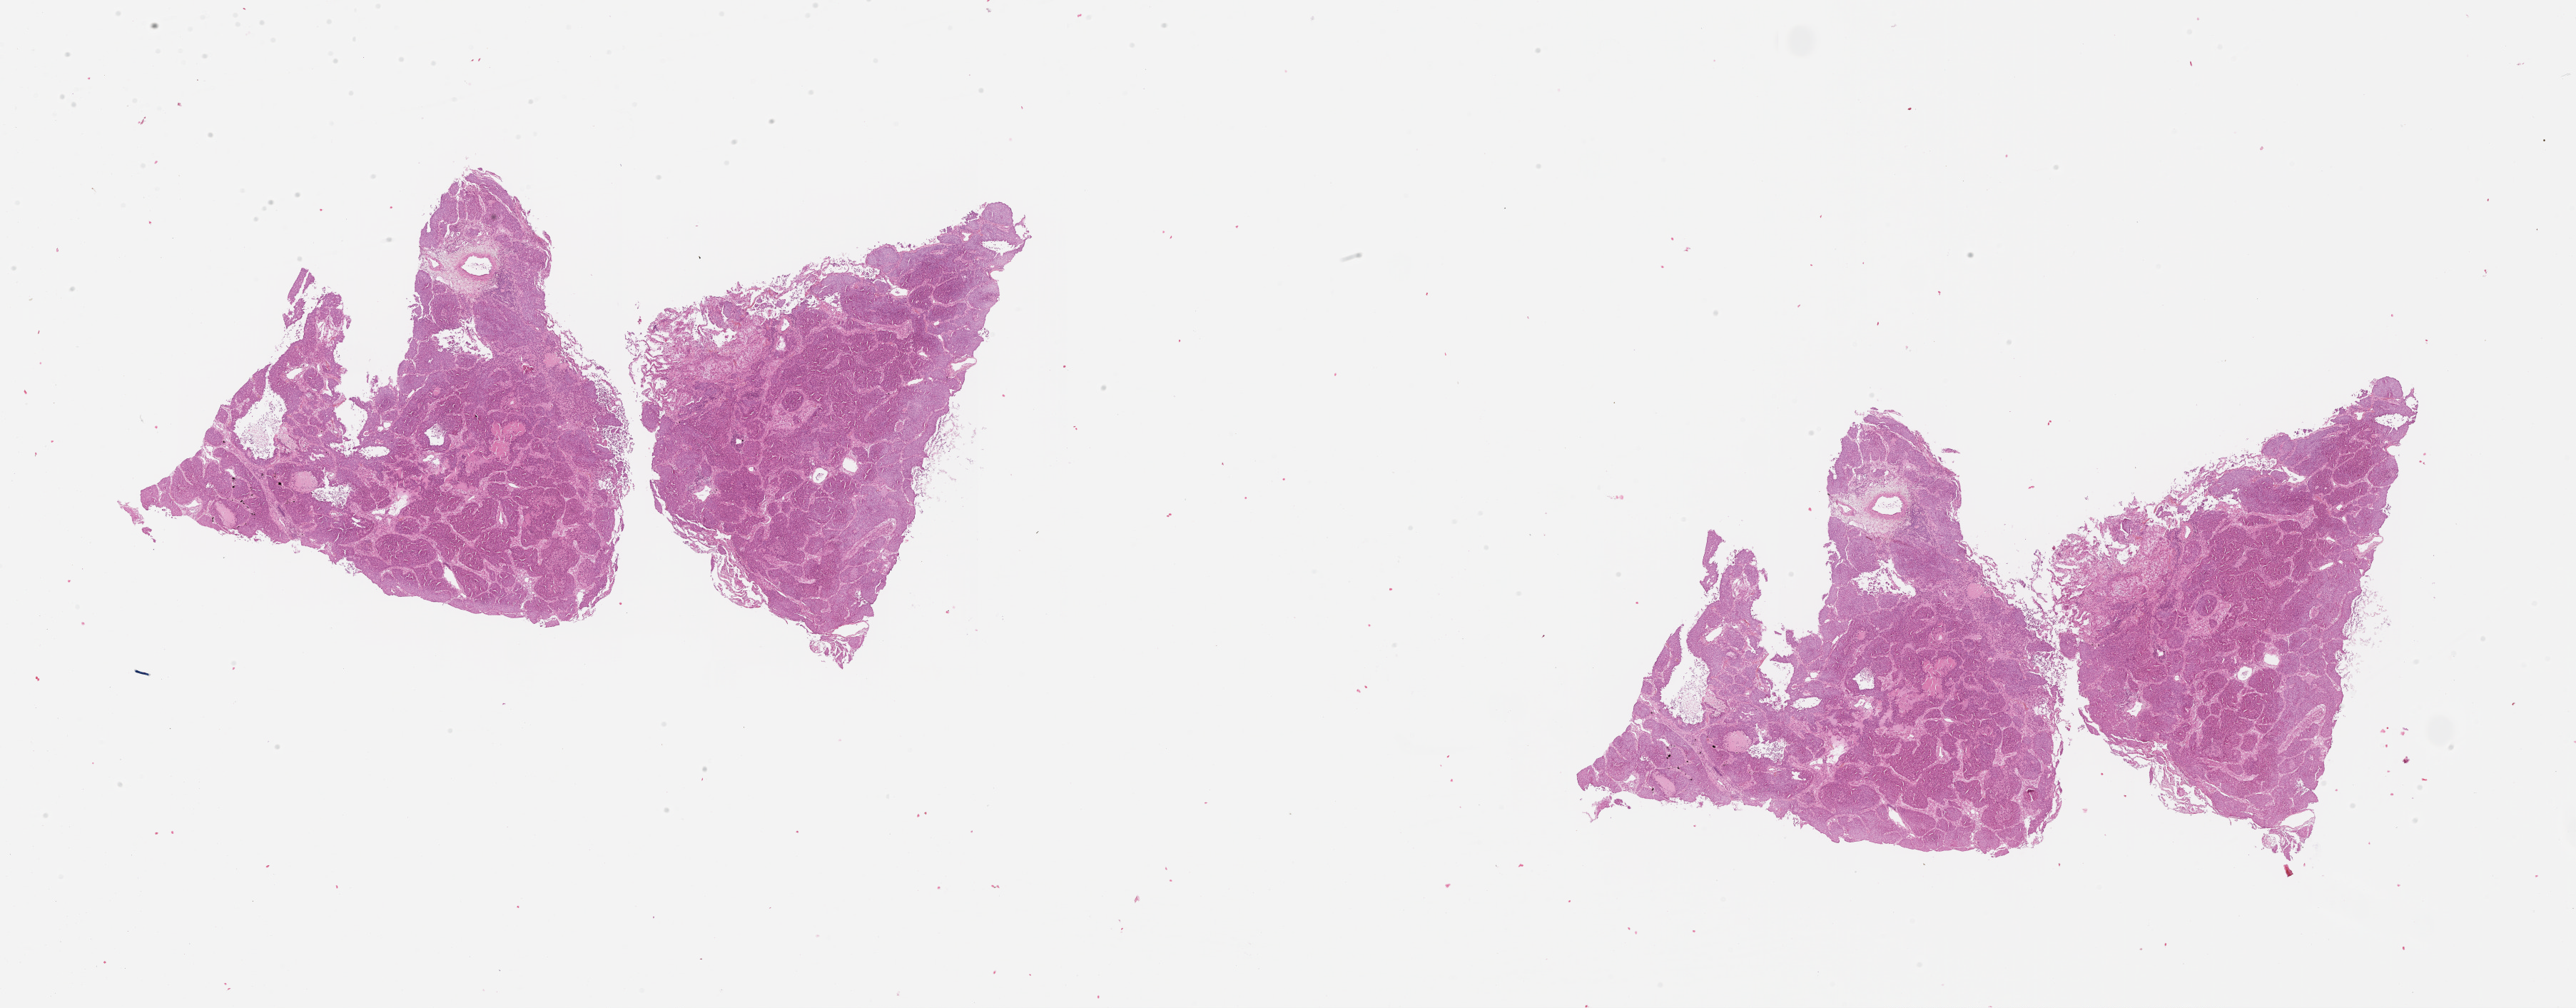
H&E whole-slide image, whole scanned area (about 29.1 x 11.4 mm) shown as a low-resolution overview; lung, tissue type not recorded.
Patient diagnosis (cohort enrolment): lung adenocarcinoma (lung).